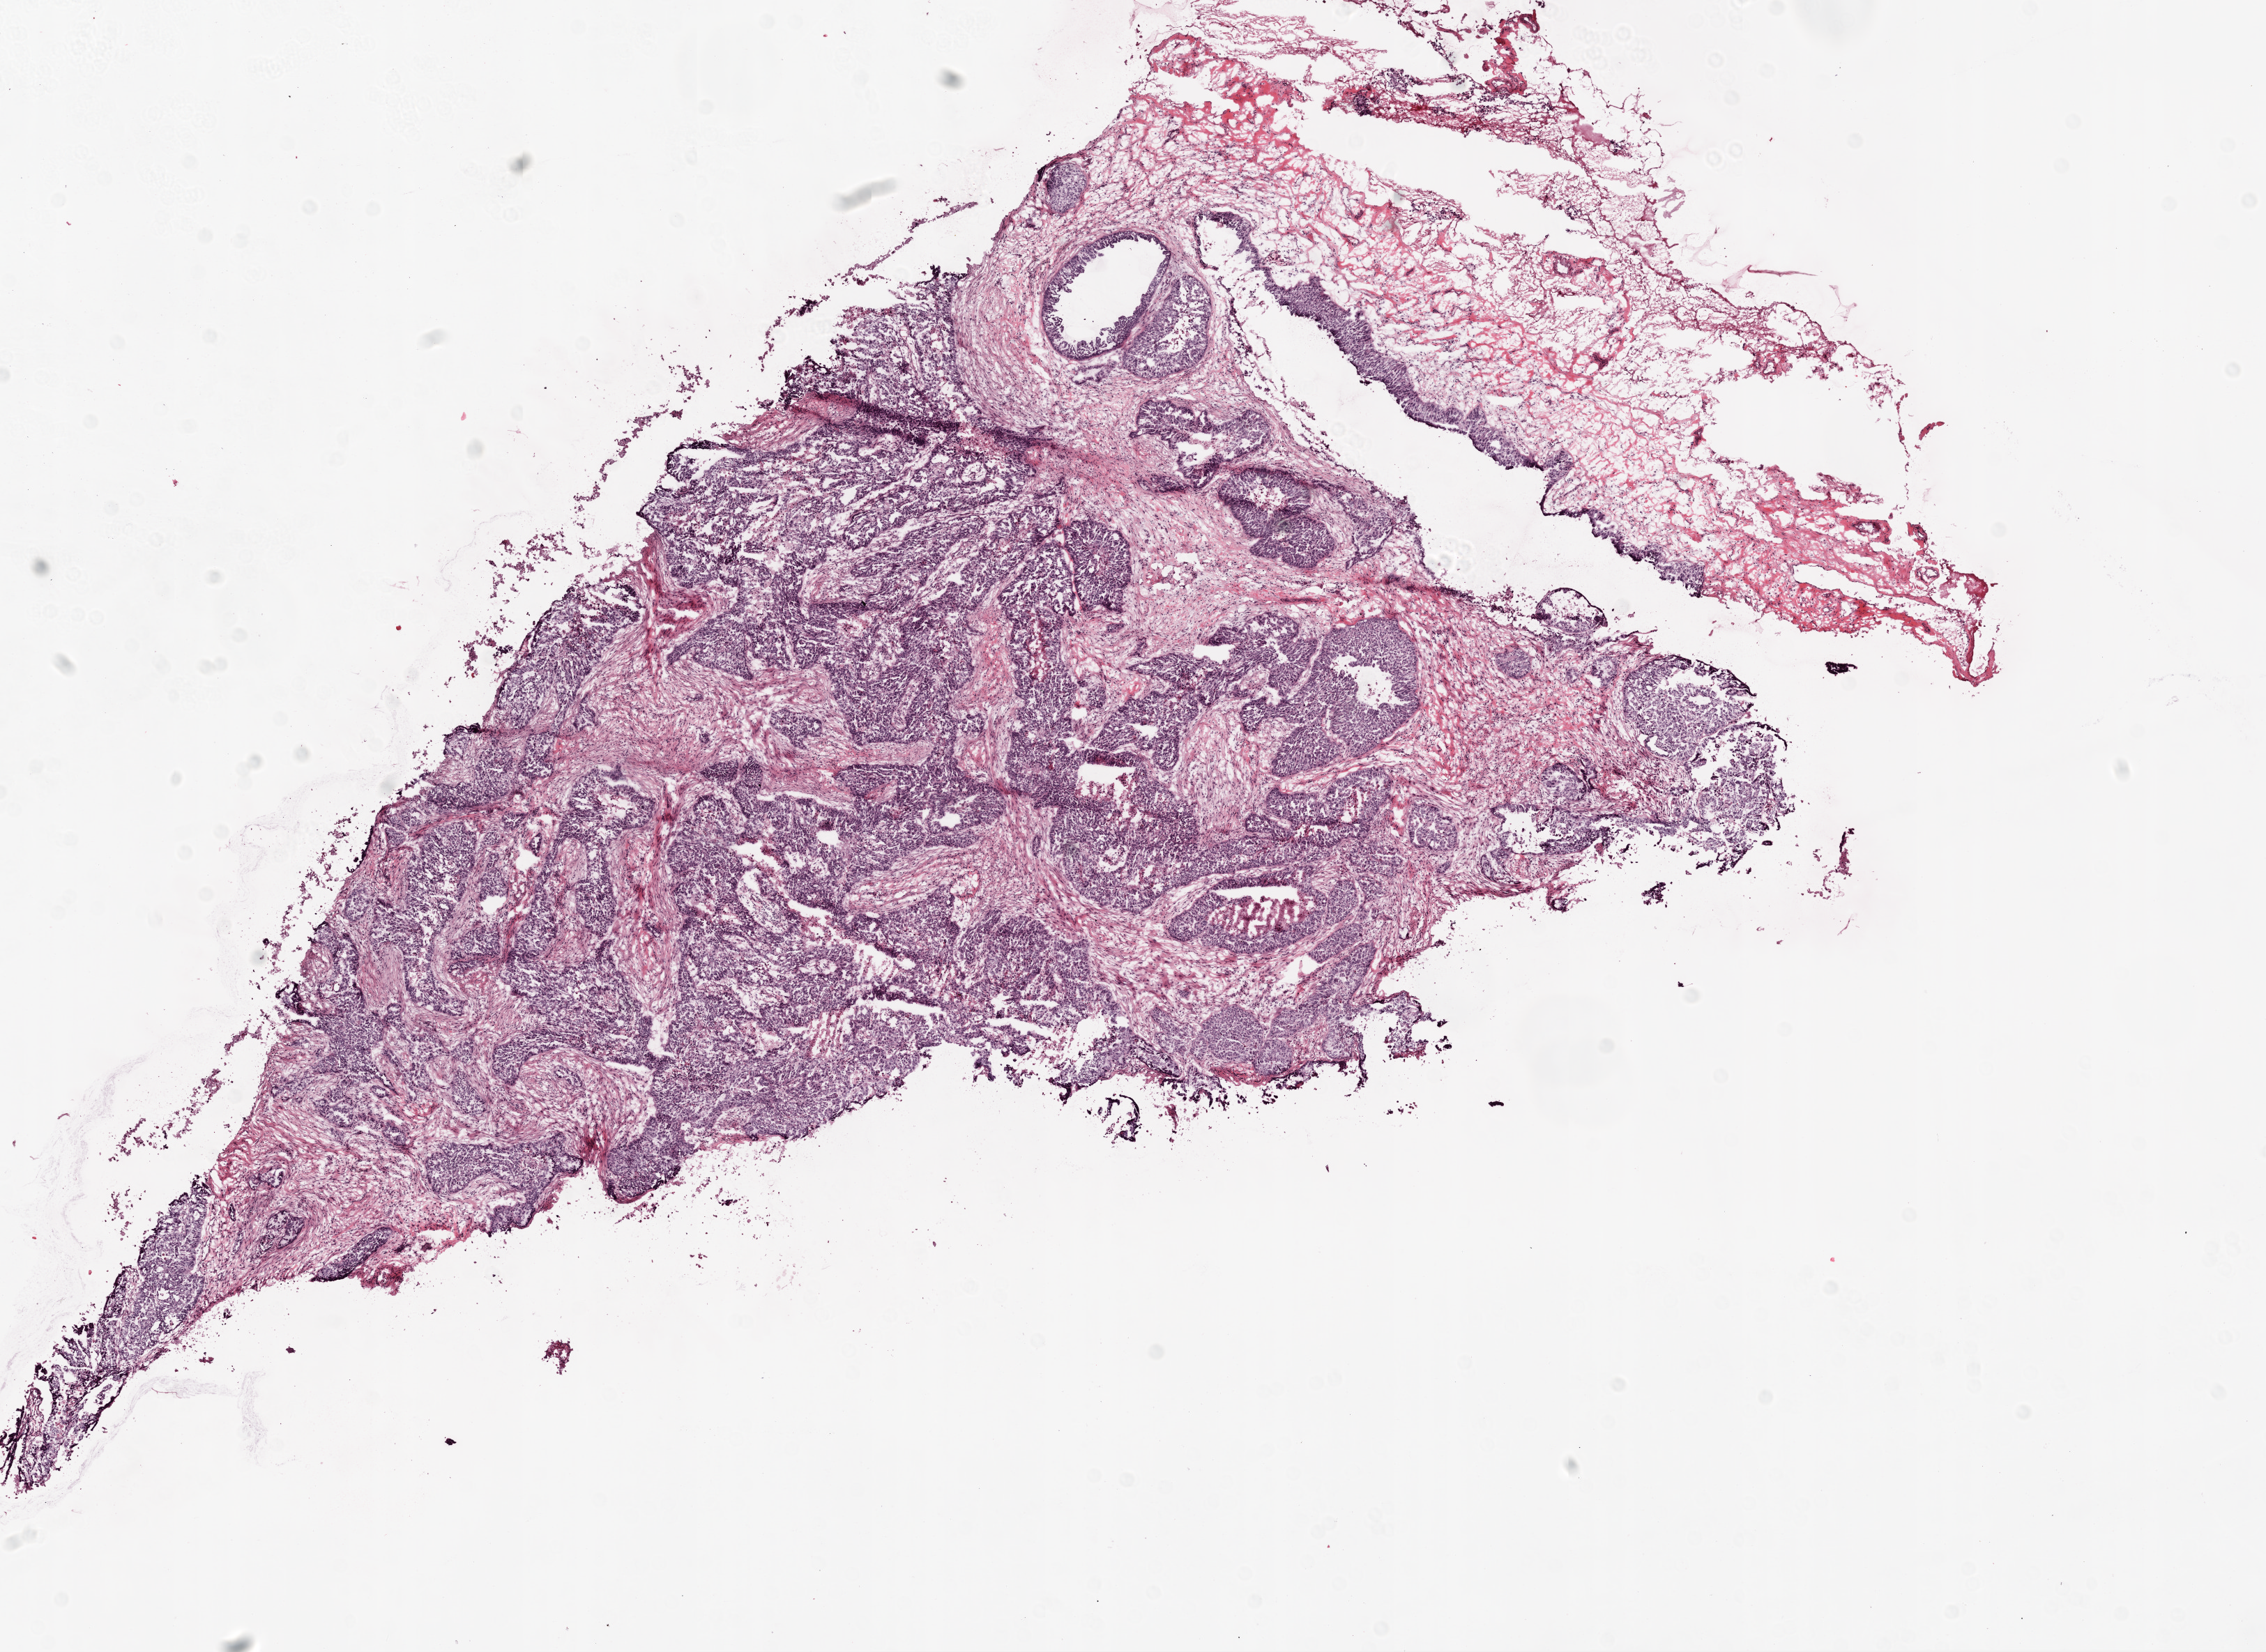
Hematoxylin and eosin (H&E) stained whole-slide image, low-resolution overview of the scanned area, about 13.0 x 9.5 mm (from a 20x scan), frozen section from the top of the tissue portion, ovary, primary tumour sample. Female, age 74 years at initial diagnosis. Histologic grade: G2 (moderately differentiated). Slide review estimates, as recorded: tumour cells 55%, tumour nuclei 90%, normal cells 0%, stromal cells 40%, necrosis 5%. Inflammatory infiltration, as recorded: lymphocyte infiltration 2%.
* pathologic diagnosis: Serous cystadenocarcinoma, NOS
* FIGO stage: IIIC